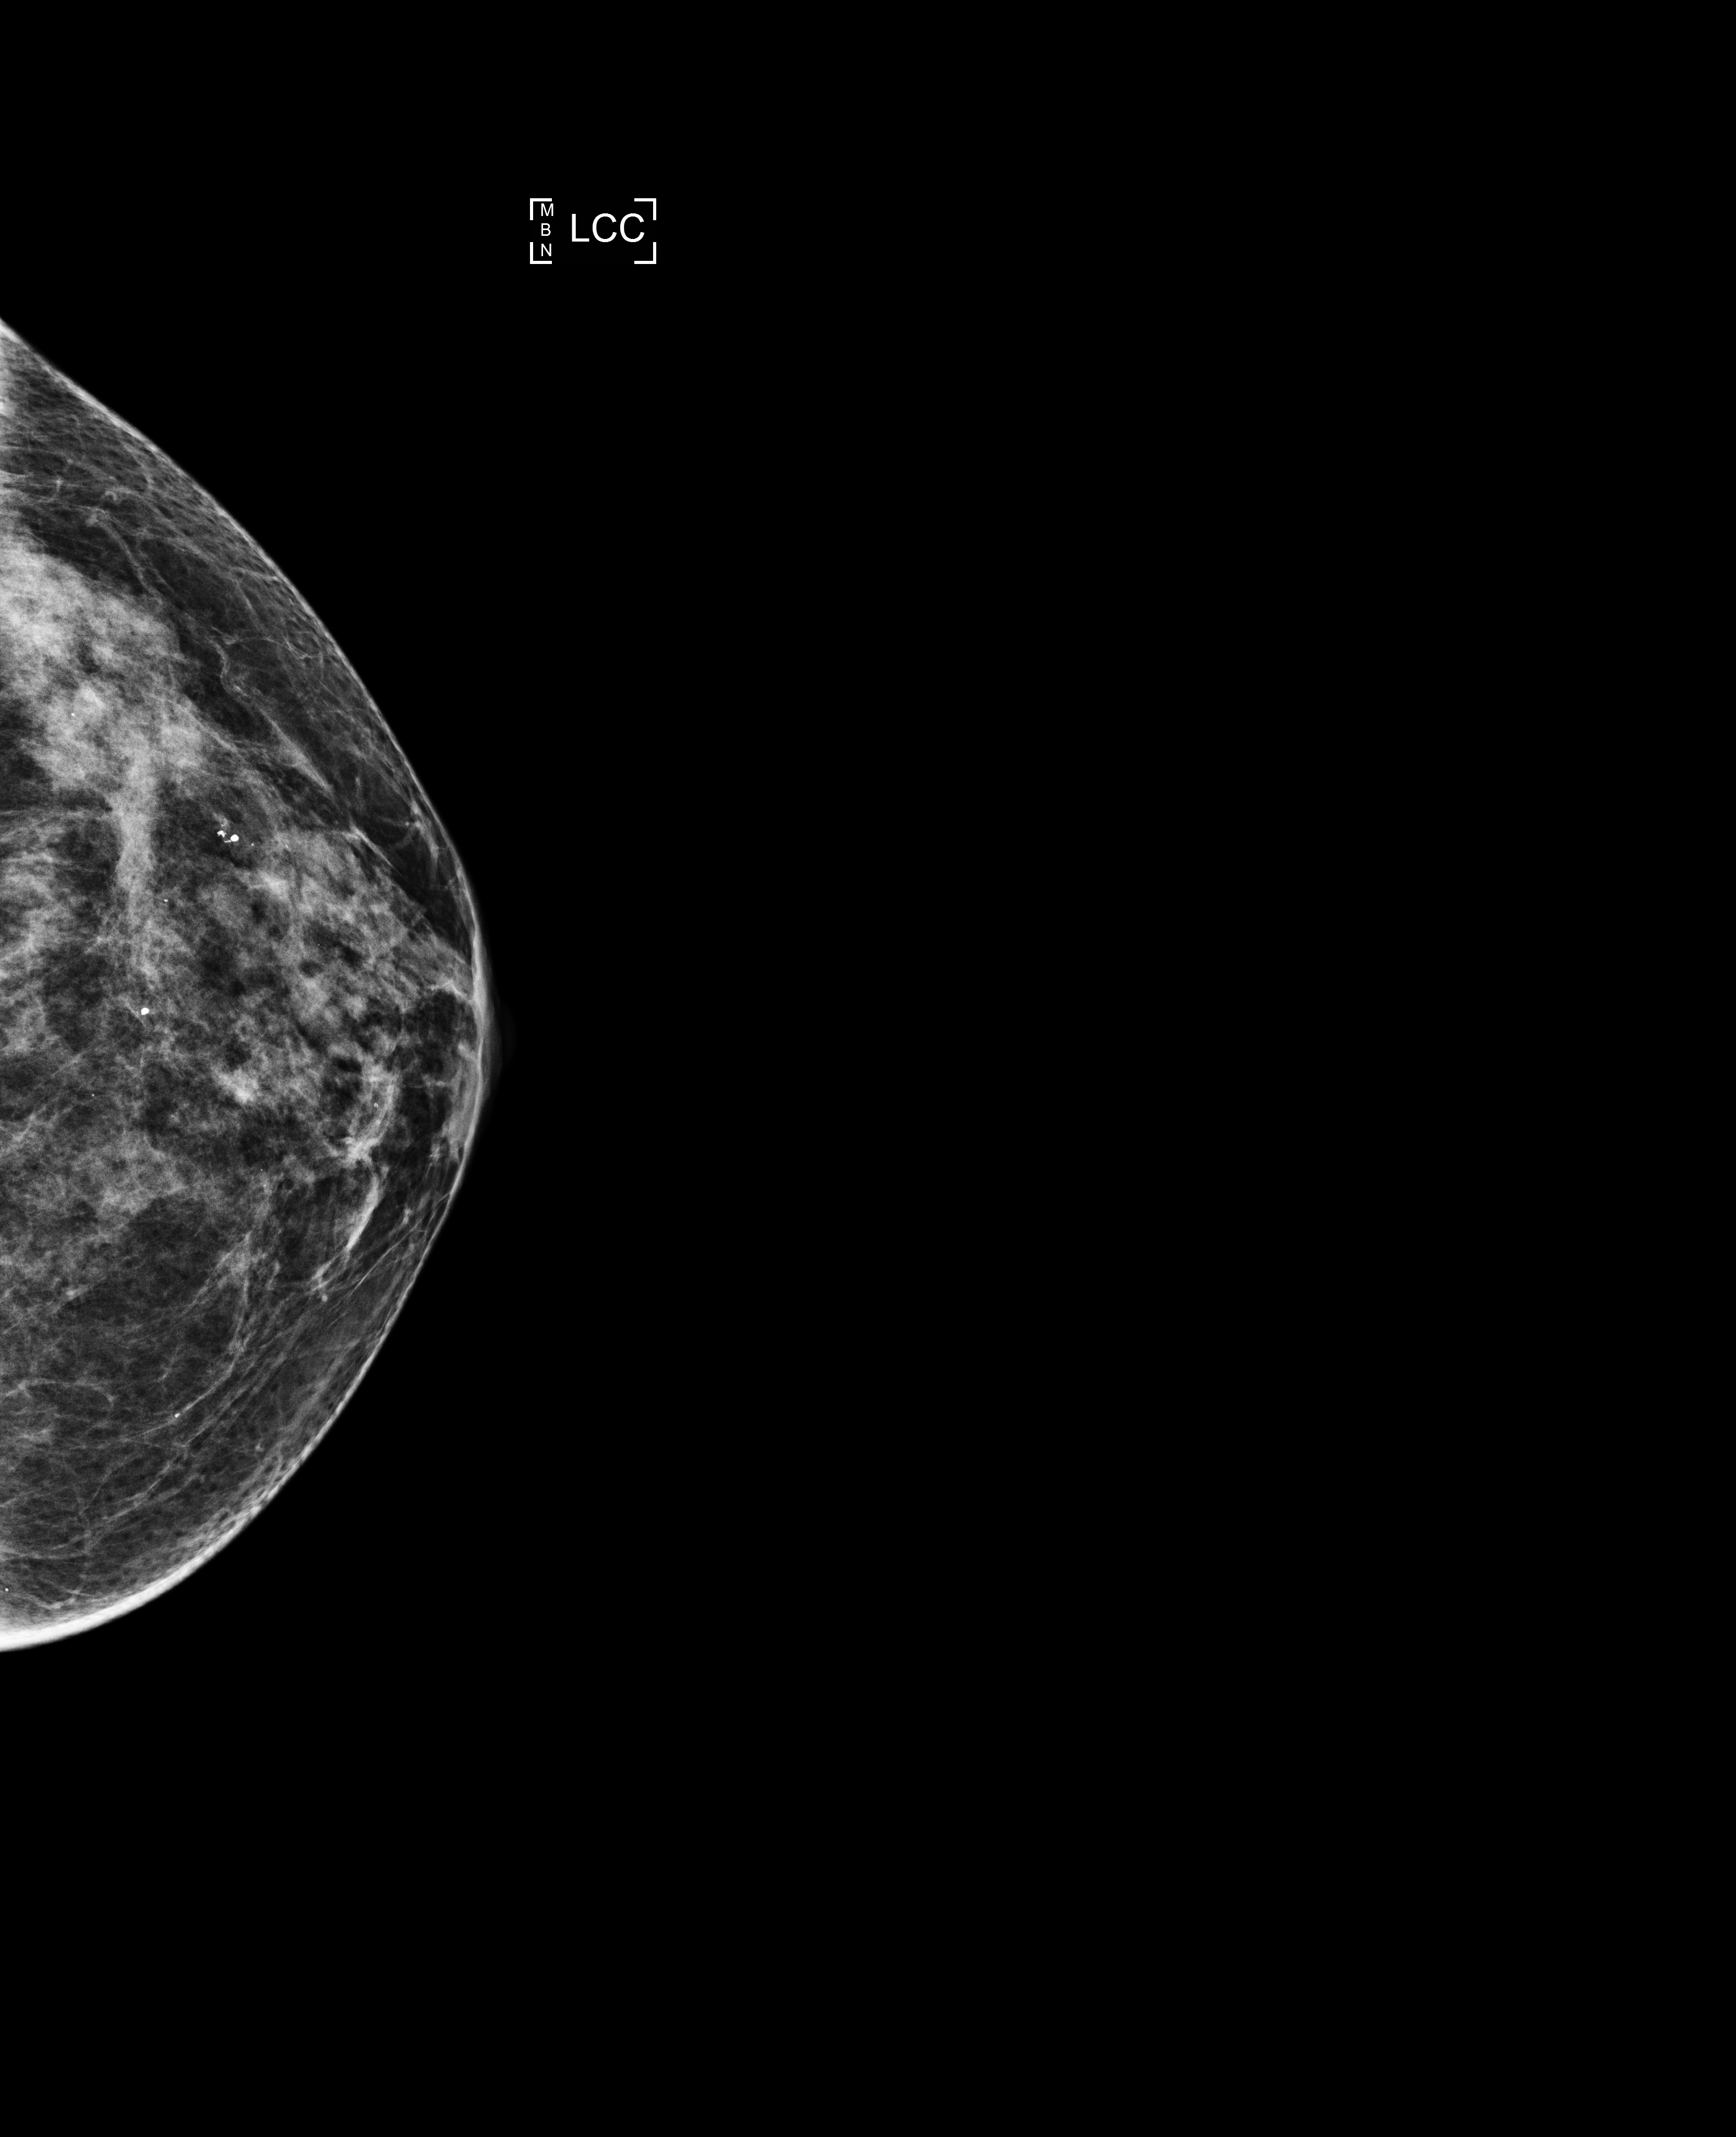
Annual screening mammography examination; compressed breast thickness 48 mm; system: Selenia Dimensions. Patient aged 75 years (female).
Image type: full-field digital mammogram. Breast: left. Projection: craniocaudal (CC) view.